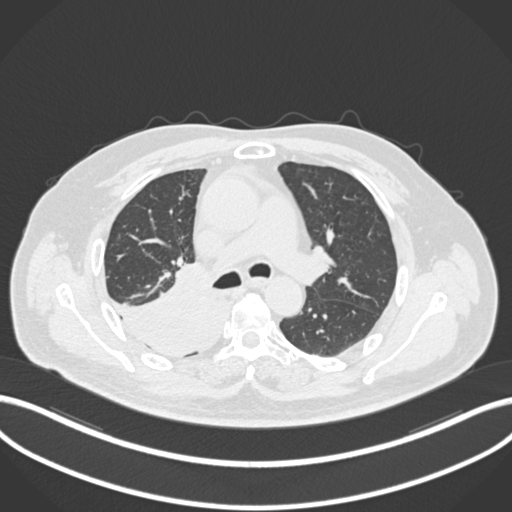
Chest CT, one axial slice. Position 126 of 218 along the scan axis. Reconstruction kernel B30f. Lung window (W 1500 / L -600 HU). 512 × 512 image matrix, field of view 400 × 400 mm. Male patient, age 68 years. Case-level facts recorded for this patient, not image findings: clinical TNM (as recorded): T2a N0 M0.
Annotated regions visible in this slice (bounding box drawn by a radiologist):
- lung tumour (recorded histology: adenocarcinoma): bounding box [x1, y1, x2, y2] px = [109, 270, 229, 360]